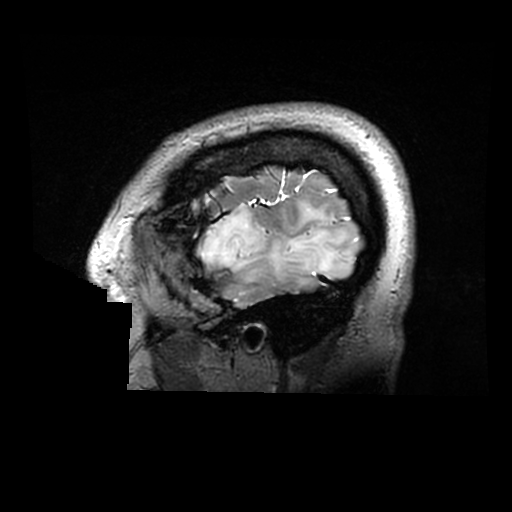
Brain MRI from a brain-tumour surgery series, one sagittal slice. Position 250 of 320 along the scan axis. 512 × 512 image matrix, field of view 240 × 240 mm. From the clinical record (not read from this slice): histopathology: Astrocytoma; WHO grade: 2; IDH mutation: yes.
Outlined on this slice (manually delineated by an expert):
- tumour: bounding box (x1, y1, x2, y2) in pixels: (199, 202, 350, 286)